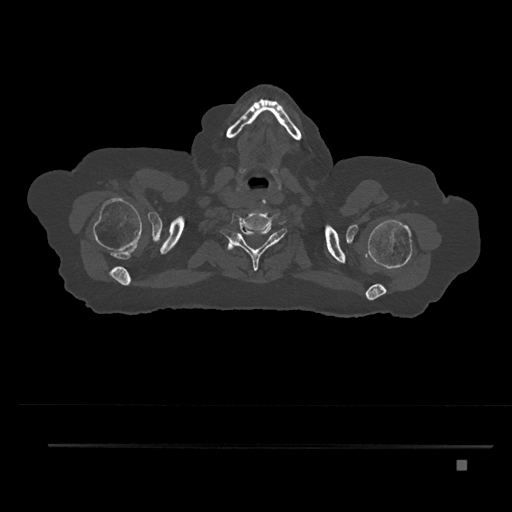
CT including the spine, one axial slice; slice 728 of 797 in the series (ordered by position); 120 kVp; bone window (W 1800 / L 400 HU); 0.5 mm slice thickness; 512 × 512 image matrix, field of view 437 × 437 mm. Patient: female, 76 years. From the clinical record (not read from this slice): primary cancer: lung; vertebrae with lytic lesions (as recorded): T11, L3.
Outlined on this slice (semi-automatically segmented with operator editing):
- T1 vertebra: bounding box (x1, y1, x2, y2) in pixels: (229, 241, 250, 255)